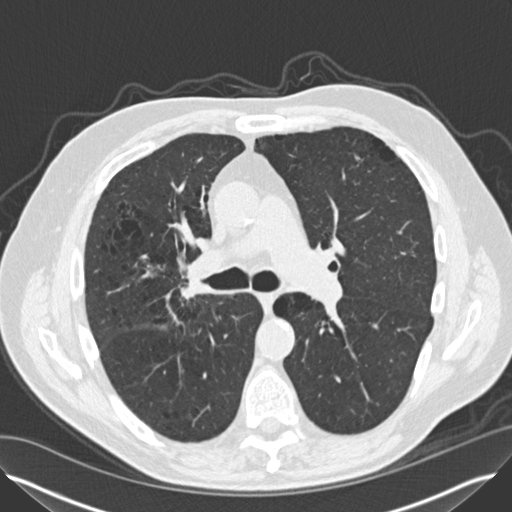
Axial slice from a low-dose chest CT screening exam. Second annual screen. Lung window (W 1500 / L -600 HU). Standard (soft-tissue) reconstruction kernel (B30f). Slice 63 of 149 in the series. Male participant, aged 65 years at enrolment. Current smoker at enrolment.
- Expert reader's lesion annotation, bounding box (x1, y1, x2, y2) in pixels: (164, 260, 221, 316).
- Screening reader's record for this exam (one nodule recorded; not confirmed to be the boxed lesion): non-calcified nodule or mass ≥4 mm, left lower lobe, 12 × 8 mm, smooth margins, soft tissue attenuation, pre-existing on the prior screen: yes; interval growth: yes.
- Note: the box lies in the patient's right hemithorax on this image, whereas the reader's record names the left lung; they may be different findings.
- Official screen result: positive, other.
- Later outcome: lung cancer diagnosed 67 days after this screen — non-small cell carcinoma, left lower lobe, right hilum, poorly differentiated (G3), stage IV (AJCC 6th edition), 5 mm at pathology.